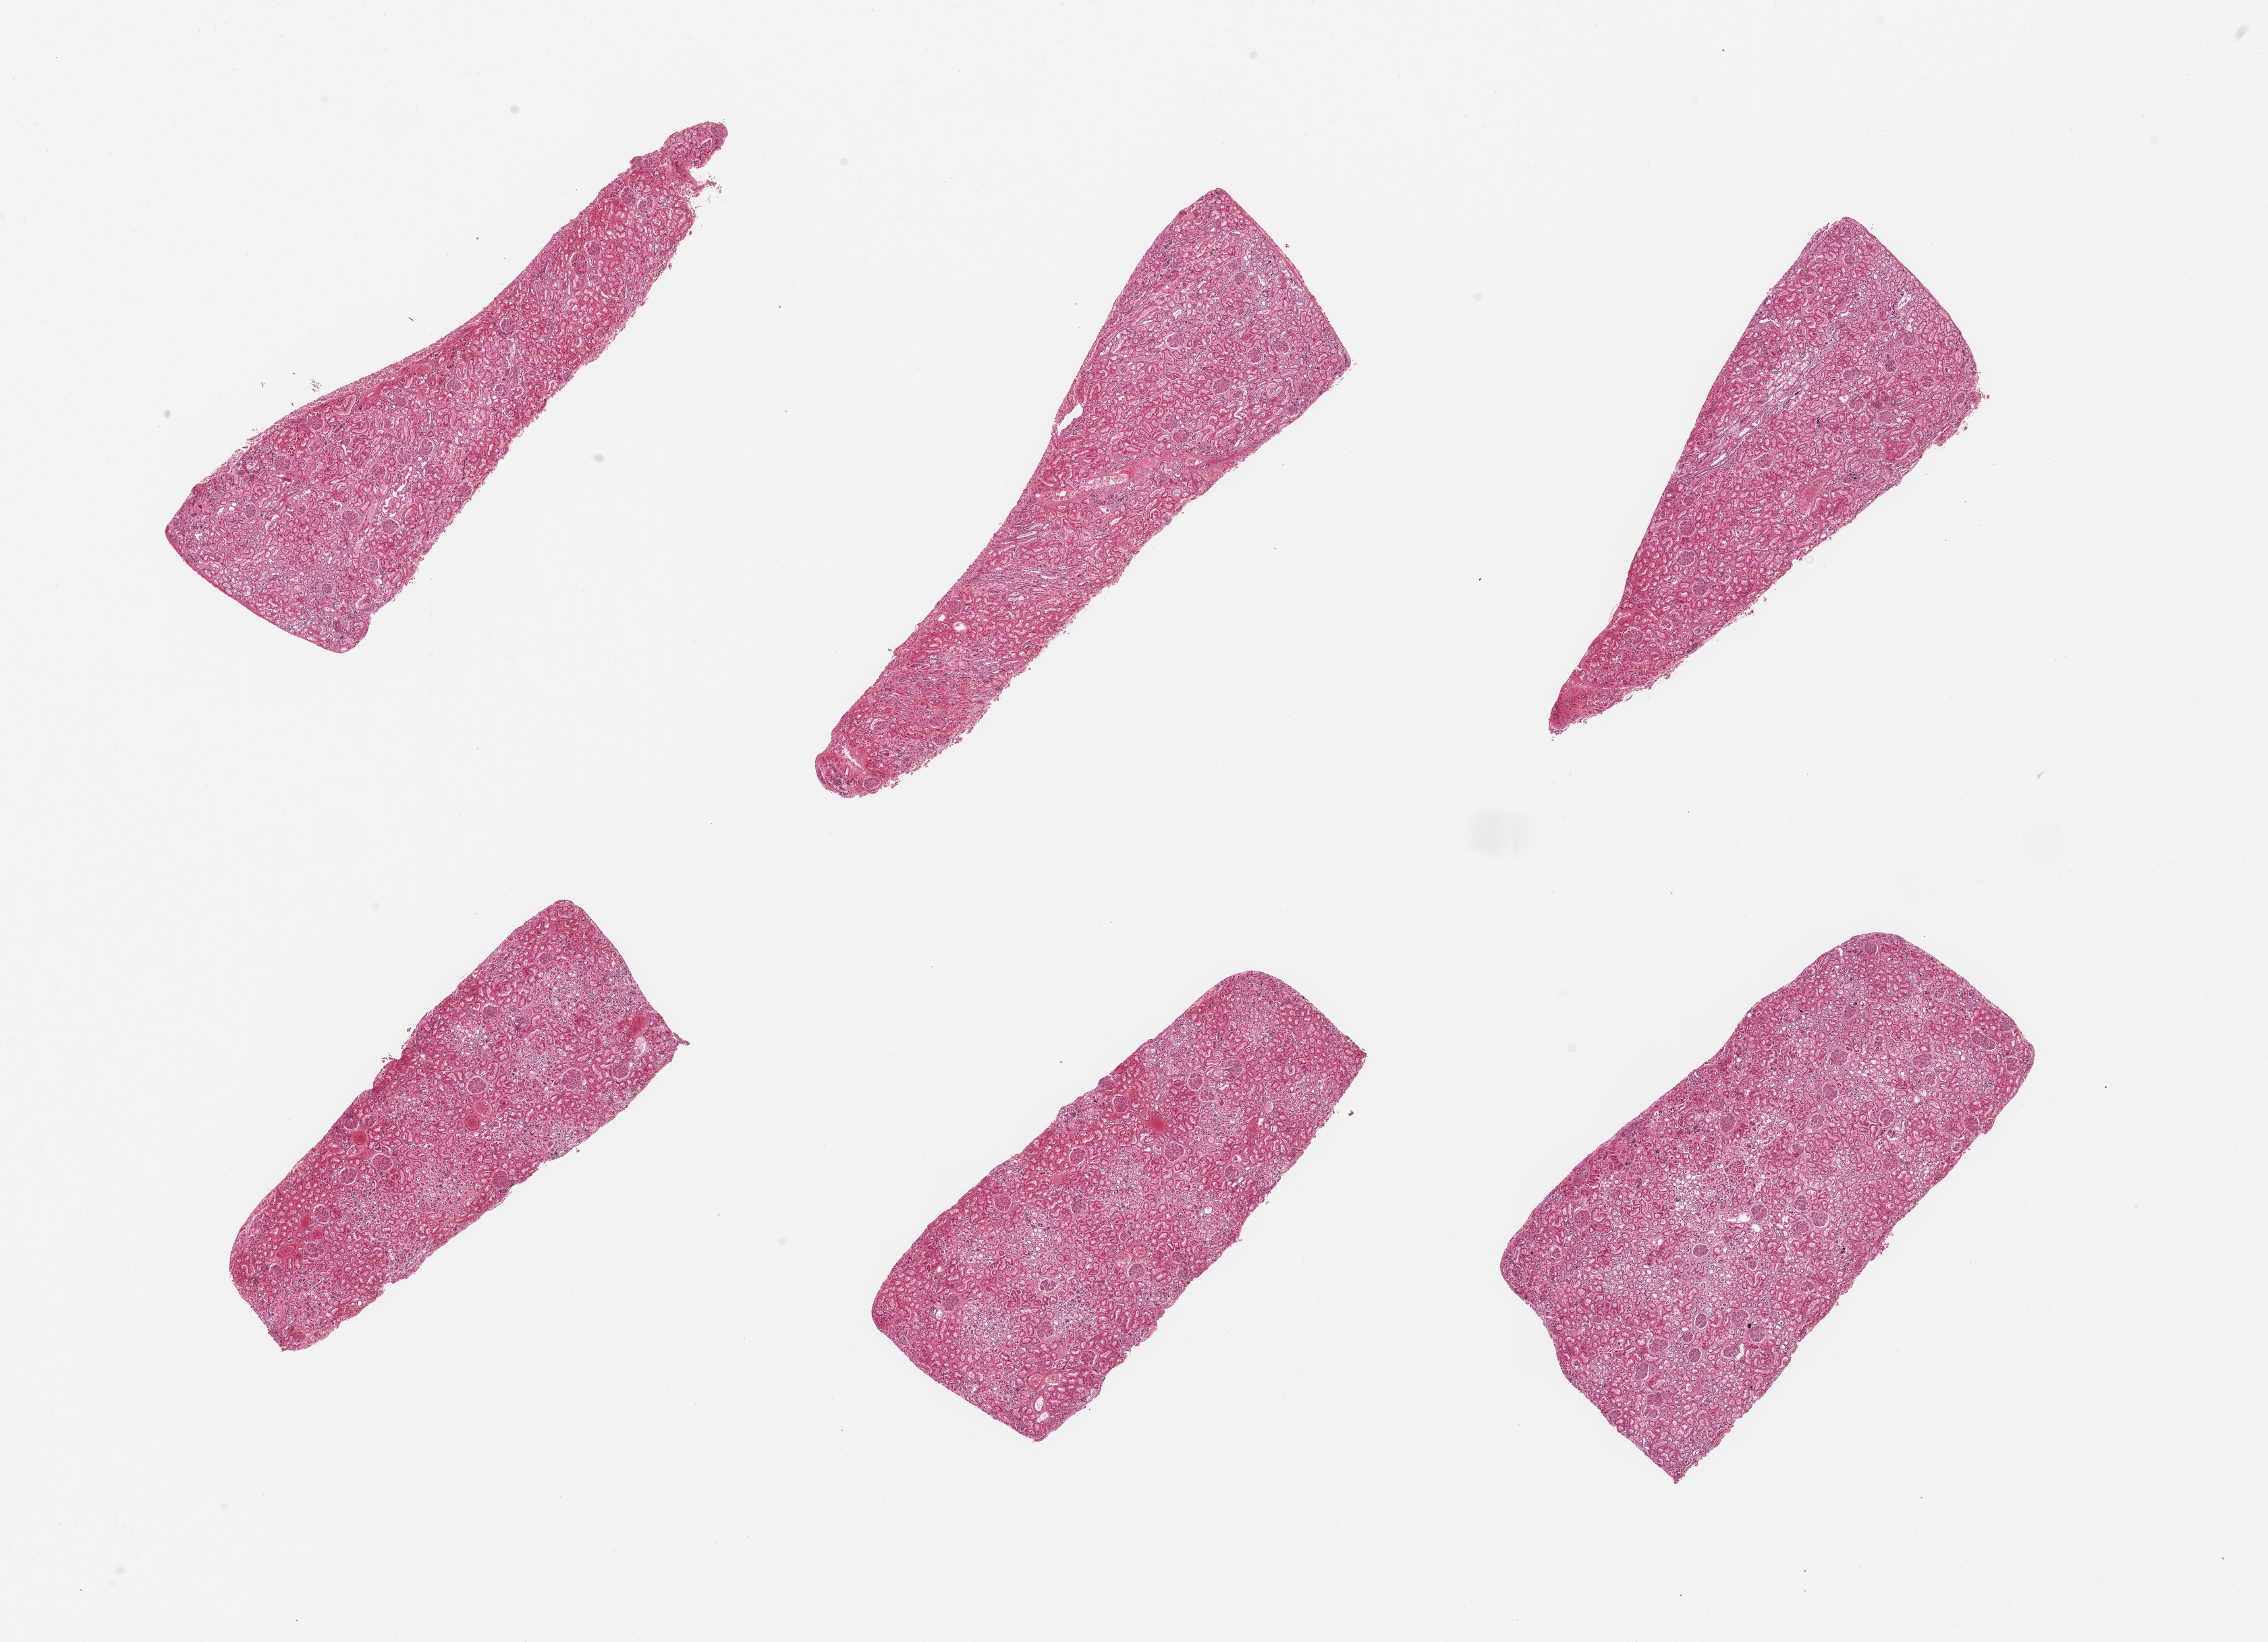
Haematoxylin and eosin whole-slide image, brightfield — shown as a low-resolution overview of the whole scanned area (about 26.6 x 19.2 mm, acquisition: 20x scan). PAXgene-fixed paraffin-embedded (PFPE) section. Section of renal cortex (target tissue). Donor tissue sample. Donor sex: female.
Review note (as recorded): 6 pieces; no underlying chronic disease; tubules poorly preserved.